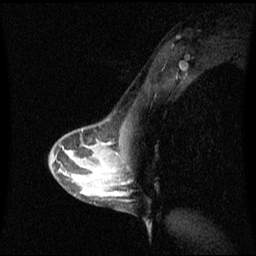
Breast MRI (dynamic contrast-enhanced), one sagittal slice. Slice 41 of 60 in the series (ordered by position). Dynamic contrast-enhanced series, image 2 of 3 at this slice position (ordered by acquisition). 1.5 T. TE 4.2 ms, TR 8.4 ms. 2.3 mm slice thickness. 256 × 256 image matrix, field of view 240 × 240 mm. Patient: female, 42 years. From the clinical record (not read from this slice): setting: breast cancer imaged before/during neoadjuvant chemotherapy; receptor status: triple-negative.
Annotated regions visible in this slice (semi-automatic segmentation, software-assisted and operator-edited):
- analysis volume of interest (the breast-tissue region the enhancement analysis was run in; not a lesion): bounding box [x1, y1, x2, y2] px = [106, 156, 129, 197]
- tumour enhancement mask (voxels above the 70 % enhancement threshold inside the analysis volume of interest): [122, 182, 124, 185]